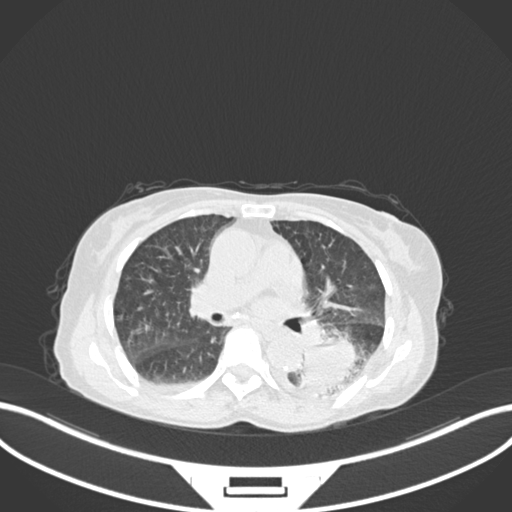
Chest CT, one axial slice; slice 96 of 233 in the series (ordered by position); reconstruction kernel B30f; lung window (W 1500 / L -600 HU); 512 × 512 image matrix, field of view 400 × 400 mm. Female patient, age 78 years. Case-level facts recorded for this patient, not image findings: clinical TNM (as recorded): T3 N0 M1.
Outlined on this slice (bounding box drawn by a radiologist):
- lung tumour (recorded histology: squamous cell carcinoma): box from (x=296, y=336) to (x=363, y=397) px